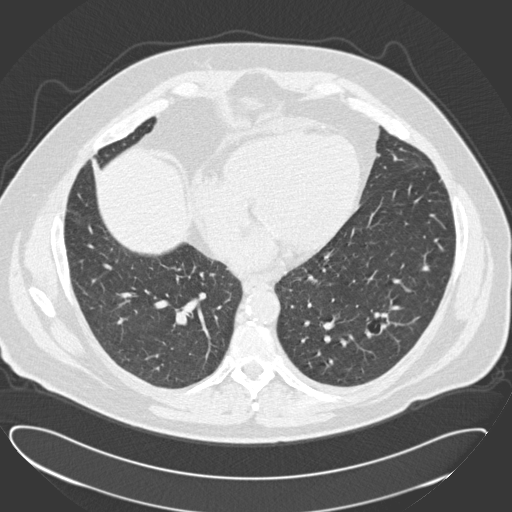
Axial slice from a low-dose chest CT screening exam. Baseline annual screen. Lung window (W 1500 / L -600 HU). Male participant, aged 57 years at enrolment.
Lesion marked by an expert reader, box from (x=356, y=301) to (x=409, y=352) px. The screening reader recorded 2 non-calcified nodules or masses ≥4 mm on this exam (left lower lobe, left lower lobe); which of them this box marks is not recorded. Later outcome: lung cancer diagnosed 791 days after this screen (after the third annual screen) — squamous cell carcinoma, NOS, left lower lobe, moderately differentiated (G2), stage IA (AJCC 6th edition), 22 mm at pathology.